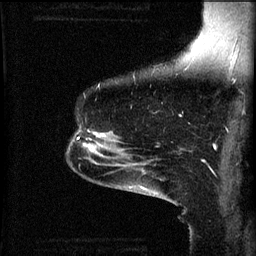
Breast MRI (dynamic contrast-enhanced), one sagittal slice. Slice 43 of 60 in the series (ordered by position). 3 images stored at this slice position (order not interpretable as contrast timing). 1.5 T. TE 4.2 ms, TR 8.2 ms. 2 mm slice thickness. 256 × 256 image matrix. Patient: female, 49 years.
Structures marked on this image (semi-automatic segmentation, software-assisted and operator-edited):
- analysis volume of interest (the breast-tissue region the enhancement analysis was run in; not a lesion): bounding box [x1, y1, x2, y2] px = [68, 130, 113, 159]
- tumour enhancement mask (voxels above the 70 % enhancement threshold inside the analysis volume of interest): [78, 132, 105, 155]